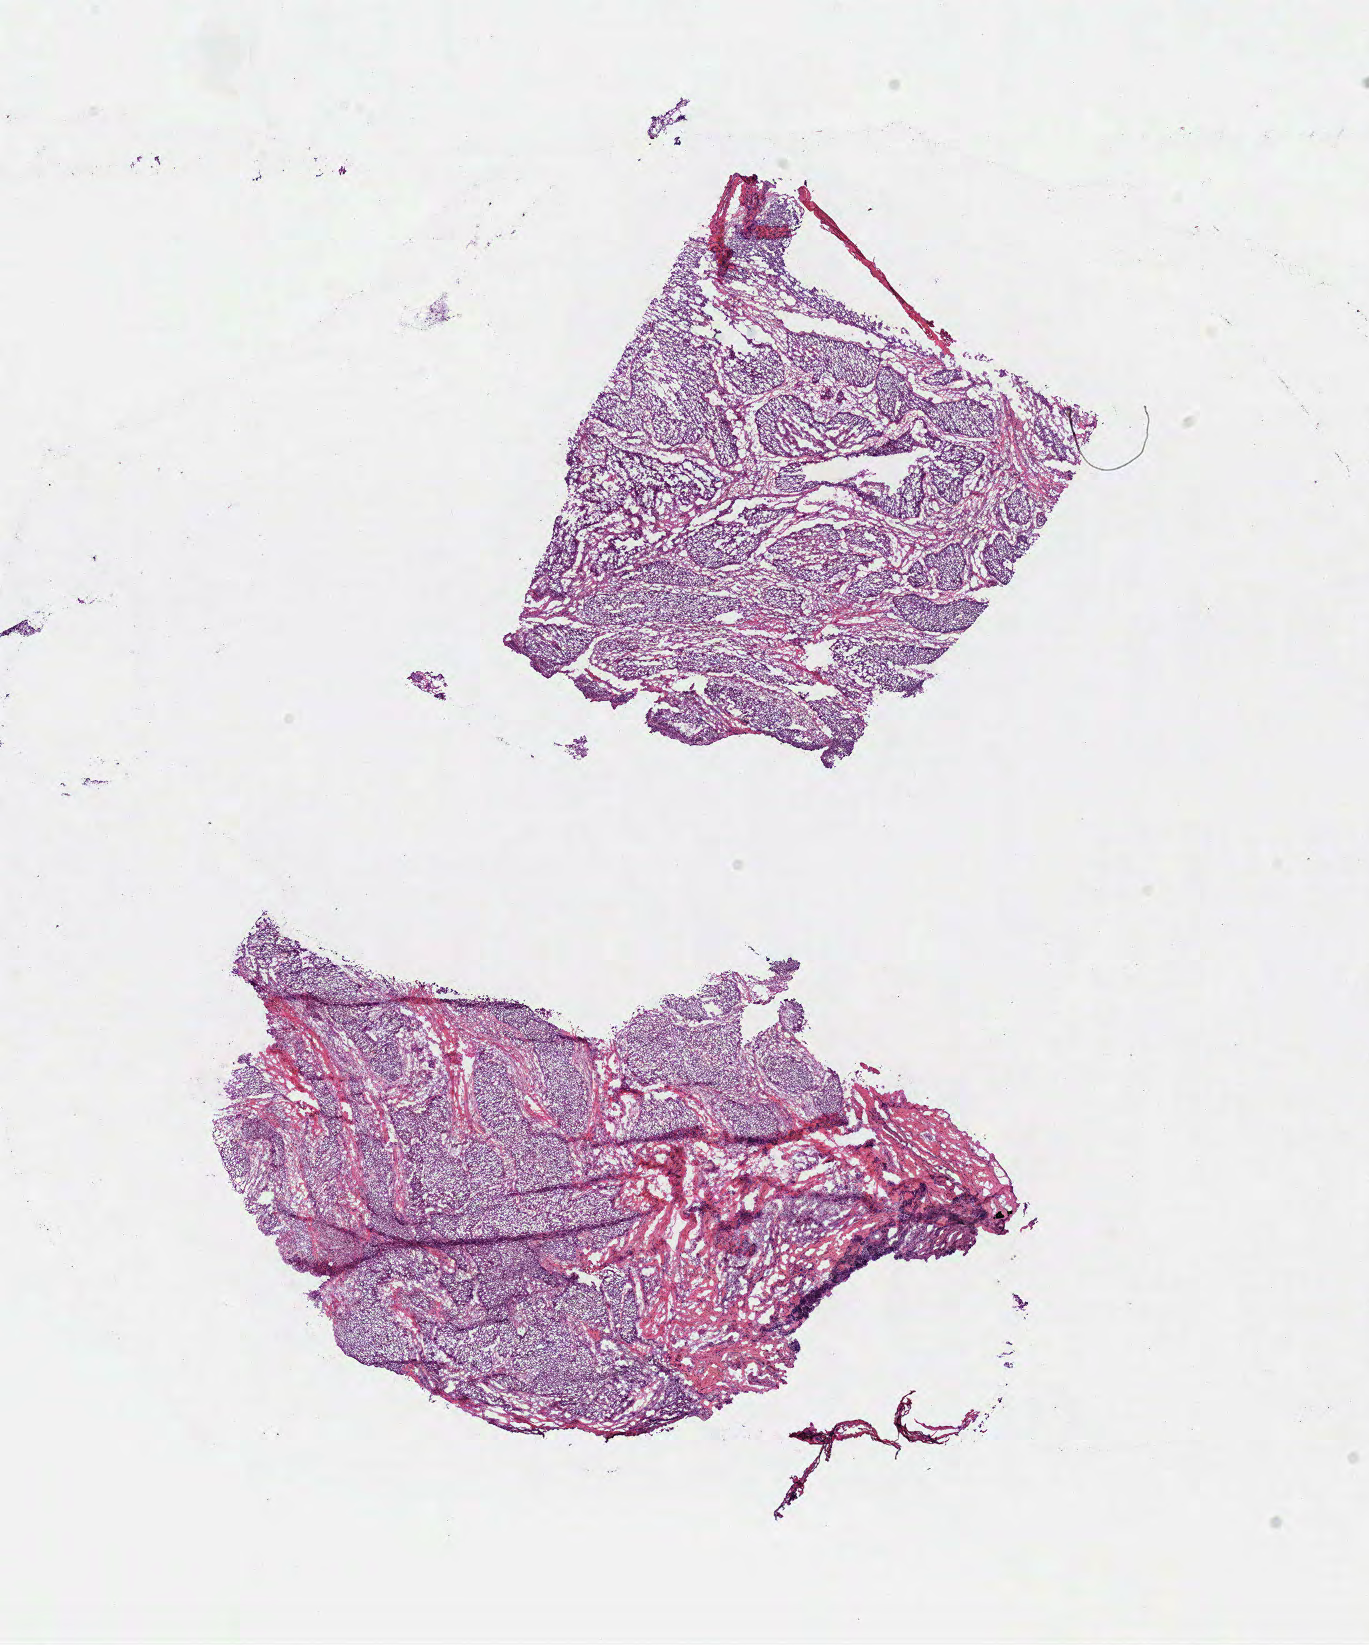
Hematoxylin and eosin (H&E) stained whole-slide image — a low-resolution overview of the entire scanned area, about 10.8 x 12.9 mm (slide scanned at 40x). Frozen section from the bottom of the tissue portion. Primary tumour sample from the head and neck. Patient: male, age at initial diagnosis 66 years. Histologic grade: G3 (poorly differentiated). Composition of this section per pathologist review: tumour cells 77%, tumour nuclei 75%, normal cells 0%, stromal cells 18%, necrosis 5%.
Histologic diagnosis: Squamous cell carcinoma, NOS (overlapping lesion of lip, oral cavity and pharynx). AJCC pathologic stage: III (7th edition). Laterality: left.